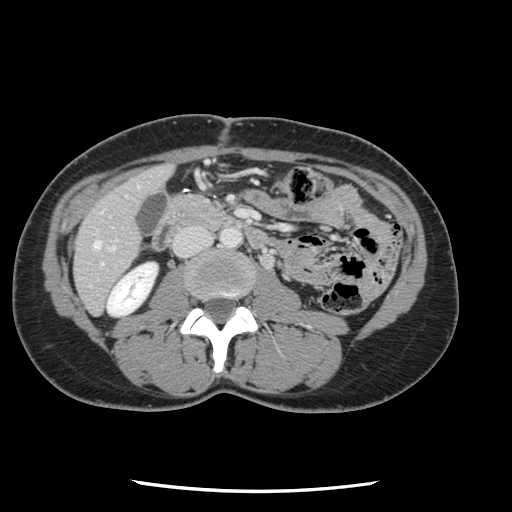
Contrast-enhanced abdominal CT, one axial slice. 120 kVp. Soft-tissue window (W 400 / L 40 HU). 2.5 mm slice thickness. 512 × 512 image matrix, field of view 330 × 330 mm. Female patient, age 43 years. From the clinical record (not read from this slice): diagnosis: colorectal cancer liver metastases, imaged before liver resection; multiple liver metastases: yes; largest metastasis: 3.4 cm; disease in both lobes: yes.
Annotated regions visible in this slice (manually delineated by an expert):
- hepatic veins: bounding box <94,241,100,248> (left, top, right, bottom; pixels)
- liver: <75,166,172,313>
- planned liver remnant (the part of the liver to remain after resection): <75,167,172,313>